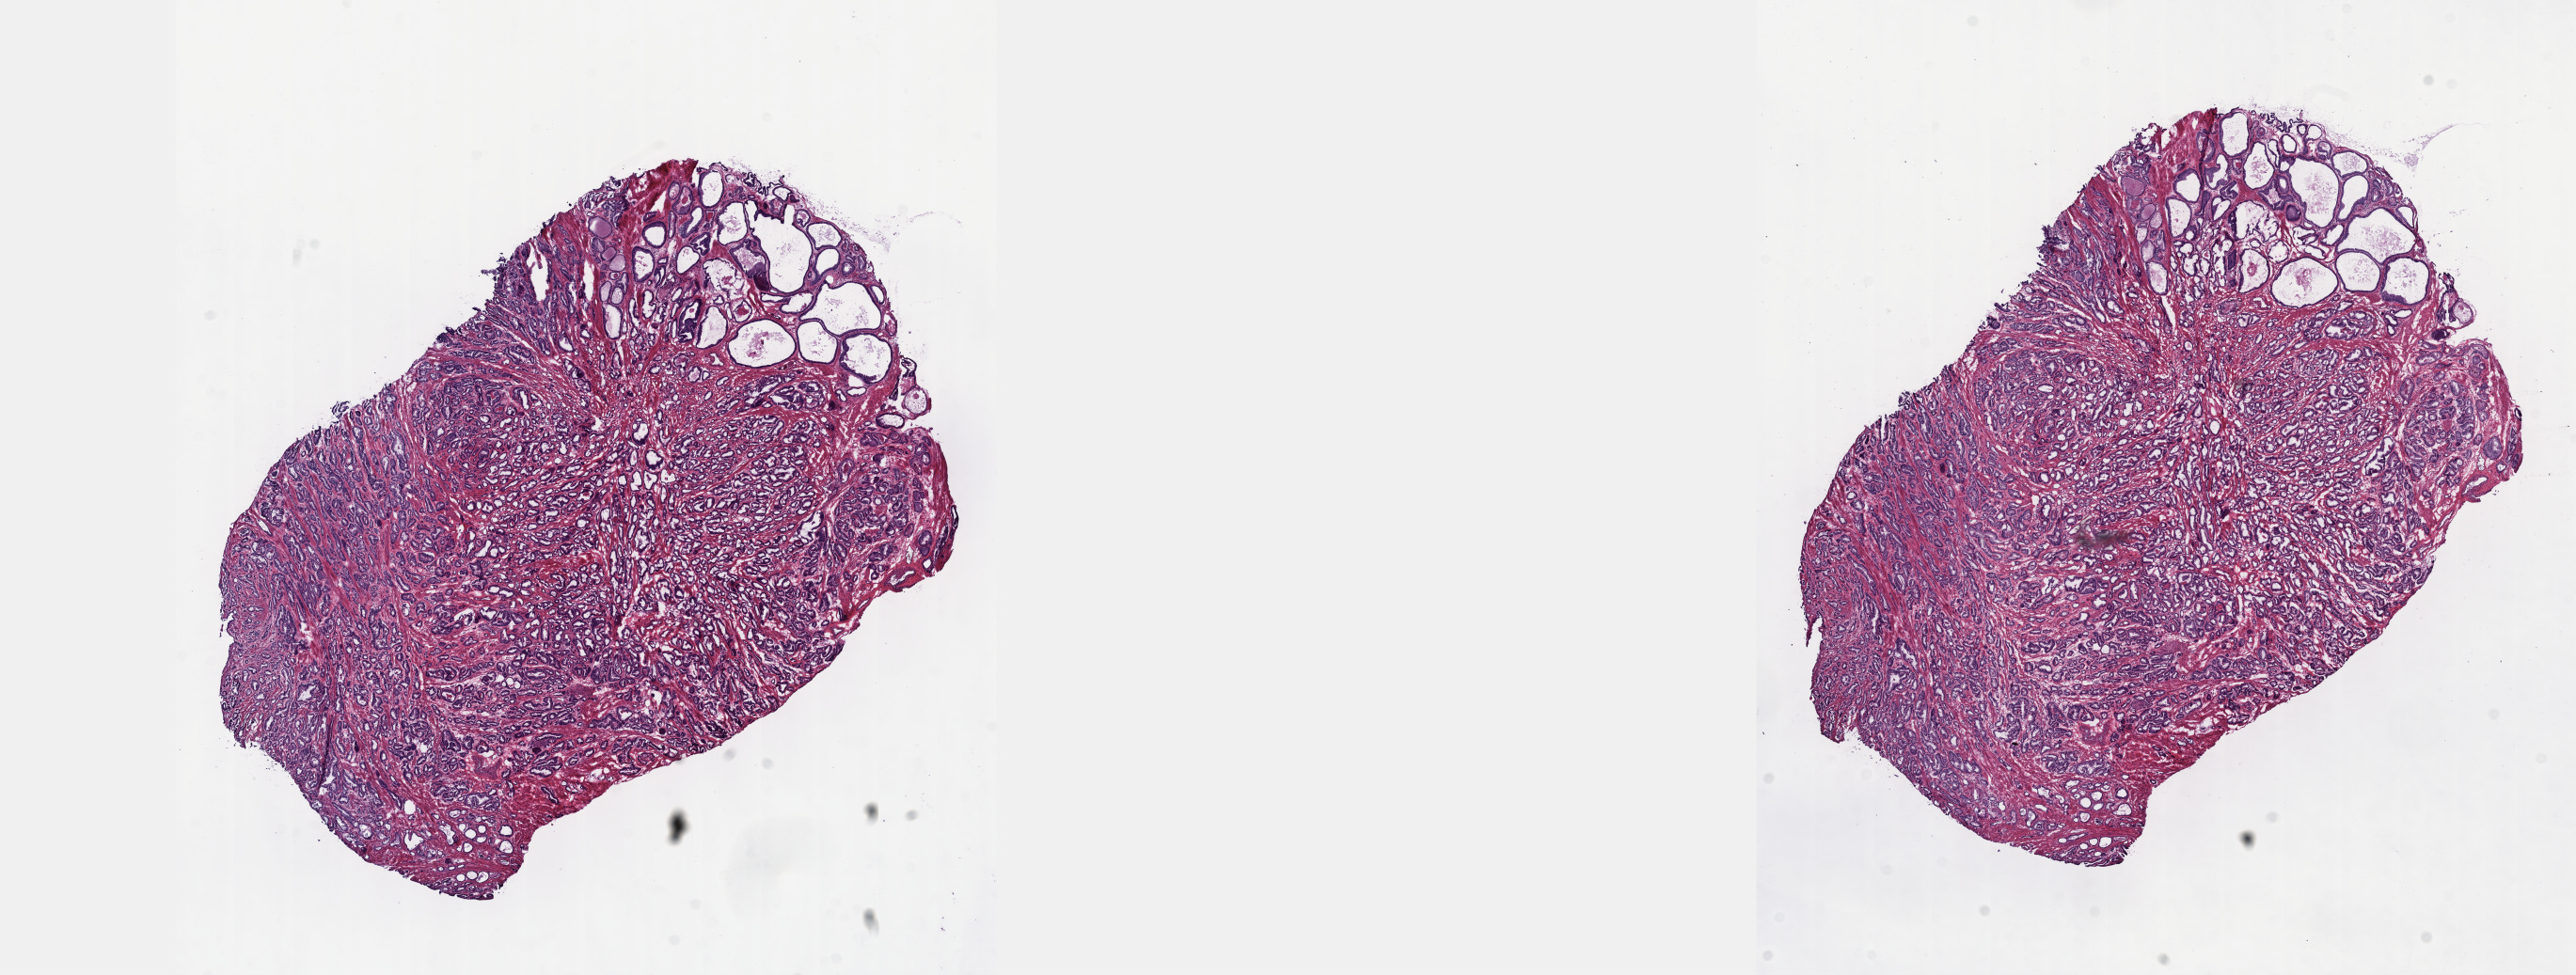
H&E-stained whole-slide image — whole scanned area (about 22.1 x 8.4 mm) shown as a low-resolution overview; frozen section from the top of the tissue portion; prostate, primary tumour sample. Patient: male, age at initial diagnosis 57 years. Gleason score: 6 (3+3). Pathologist review of this section (percent, as recorded): tumour cells 85%, tumour nuclei 70%, normal cells 5%, stromal cells 10%, necrosis 0%. Inflammatory infiltration, as recorded: lymphocyte infiltration 0%, monocyte infiltration 0%, neutrophil infiltration 0%.
Pathologic diagnosis: Adenocarcinoma, NOS.